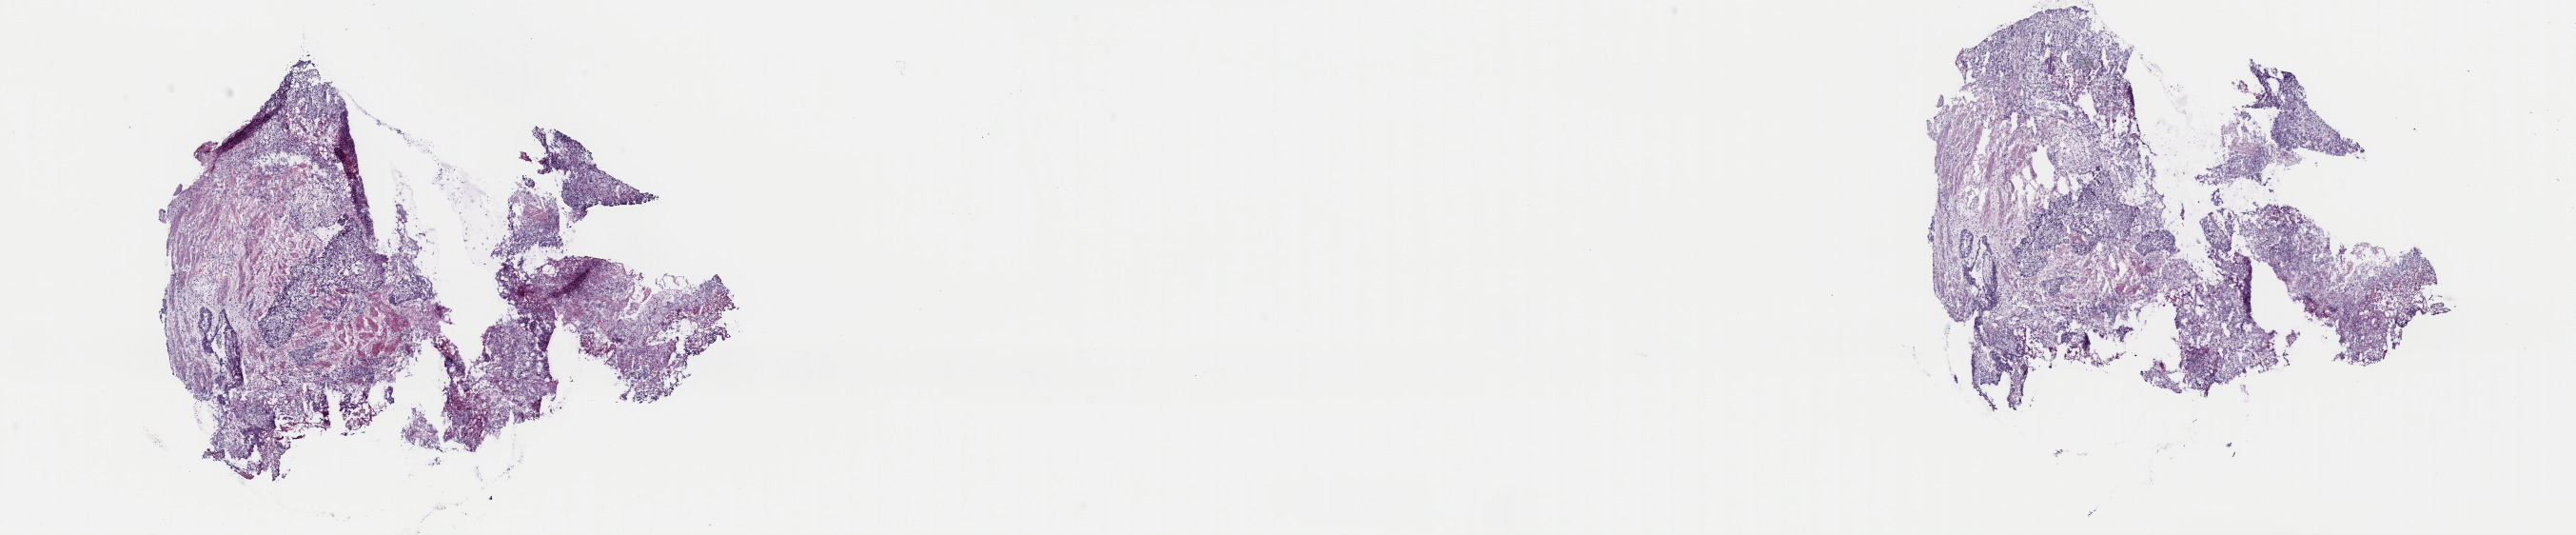
H&E whole-slide image, shown as a low-resolution overview of the whole scanned area (about 21.4 x 4.4 mm); frozen section from the top of the tissue portion; sample: primary tumour, esophagus. Male patient; age at initial diagnosis 75 years. Histologic grade: GX (grade cannot be assessed). Composition of this section per pathologist review: tumour cells 39%, tumour nuclei 60%, normal cells 0%, stromal cells 60%, necrosis 1%. Inflammatory infiltration, as recorded: lymphocyte infiltration 4%, monocyte infiltration 10%, neutrophil infiltration 1%.
Histologic diagnosis: Squamous cell carcinoma, NOS. Lymph nodes positive (case pathology): 2 of 23 examined. AJCC pathologic stage: III (7th edition).